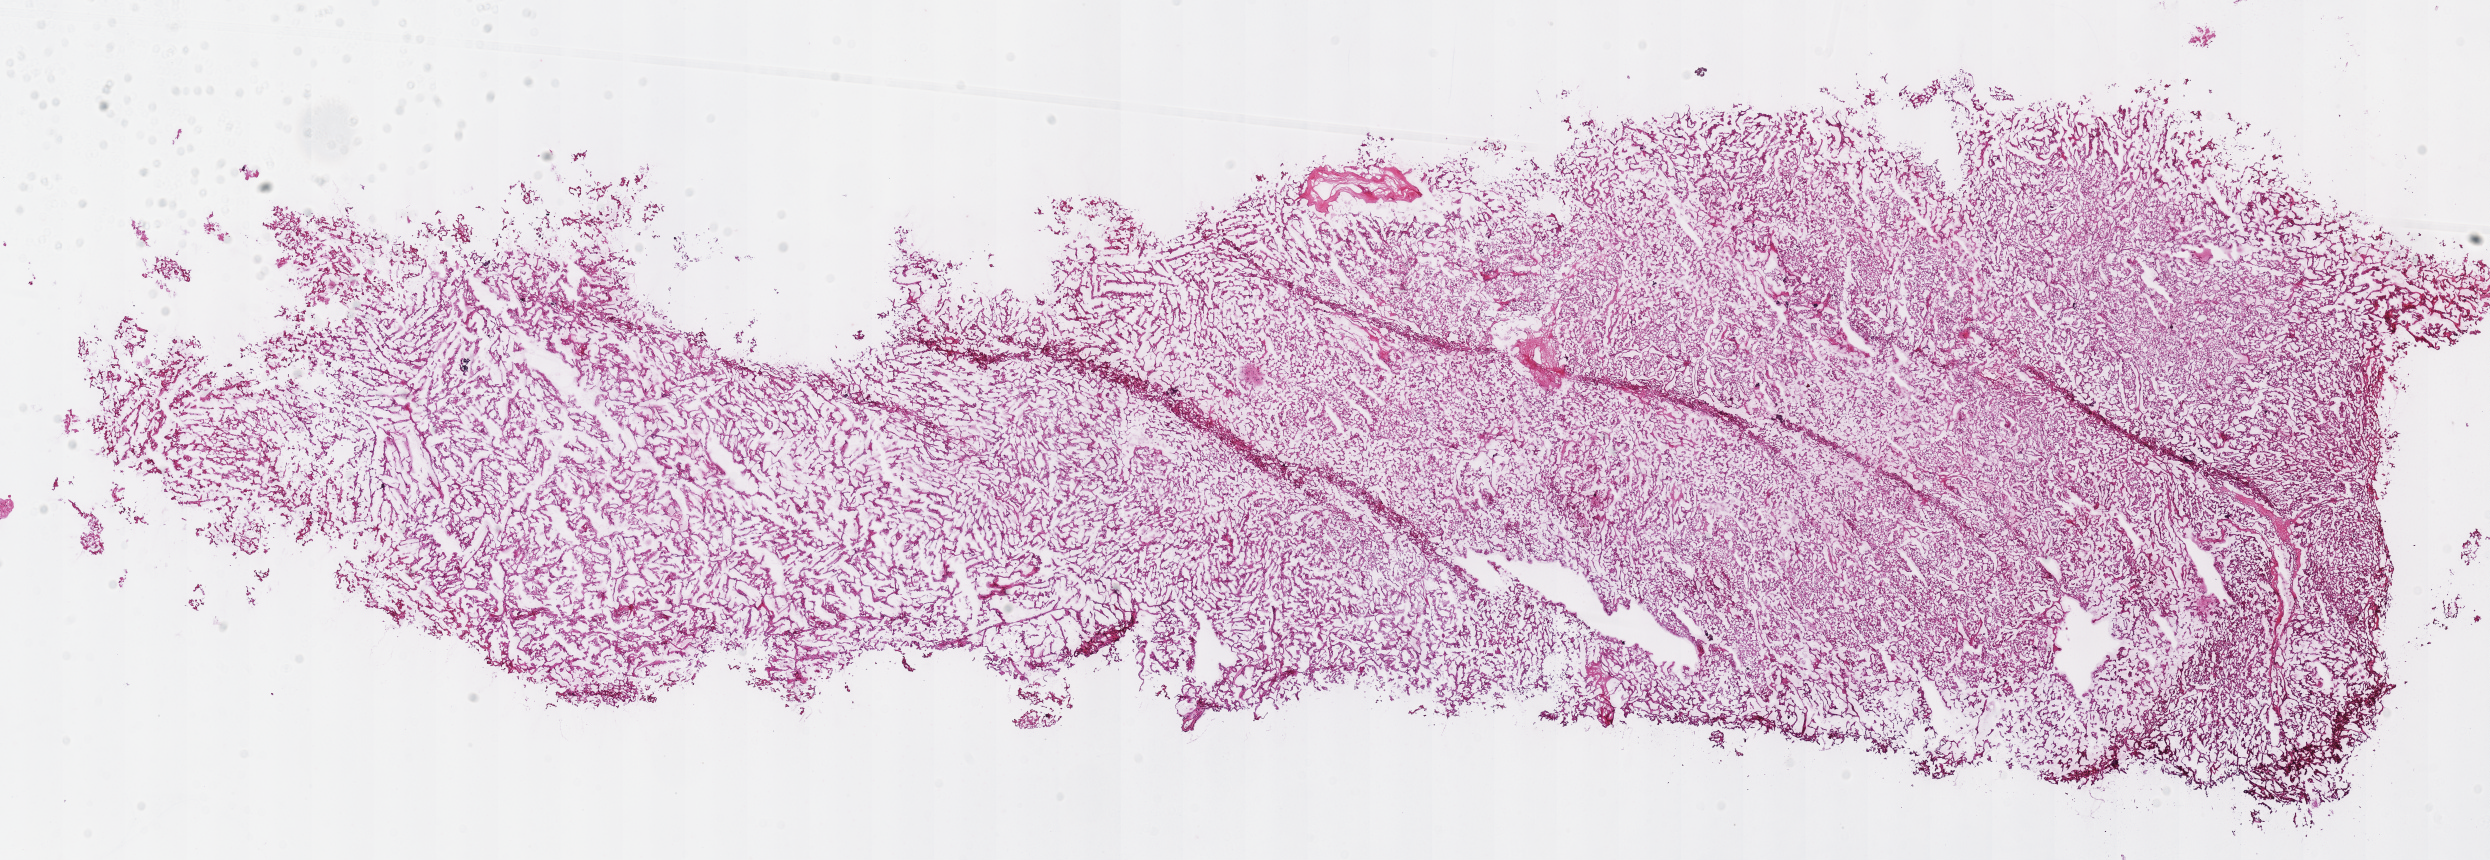
Digitized H&E tissue section (whole slide) — a low-resolution overview of the entire scanned area, about 19.6 x 6.8 mm; frozen section from the top of the tissue portion; primary tumour sample from the kidney. Male, age 42 years at initial diagnosis. Pathologist review of this section (percent, as recorded): tumour cells 90%, tumour nuclei 90%, normal cells 0%, stromal cells 10%, necrosis 0%.
Laterality: left. Histologic diagnosis: Renal cell carcinoma, chromophobe type. Lymph nodes positive (case pathology): 0 of 10 examined. AJCC pathologic stage: II.